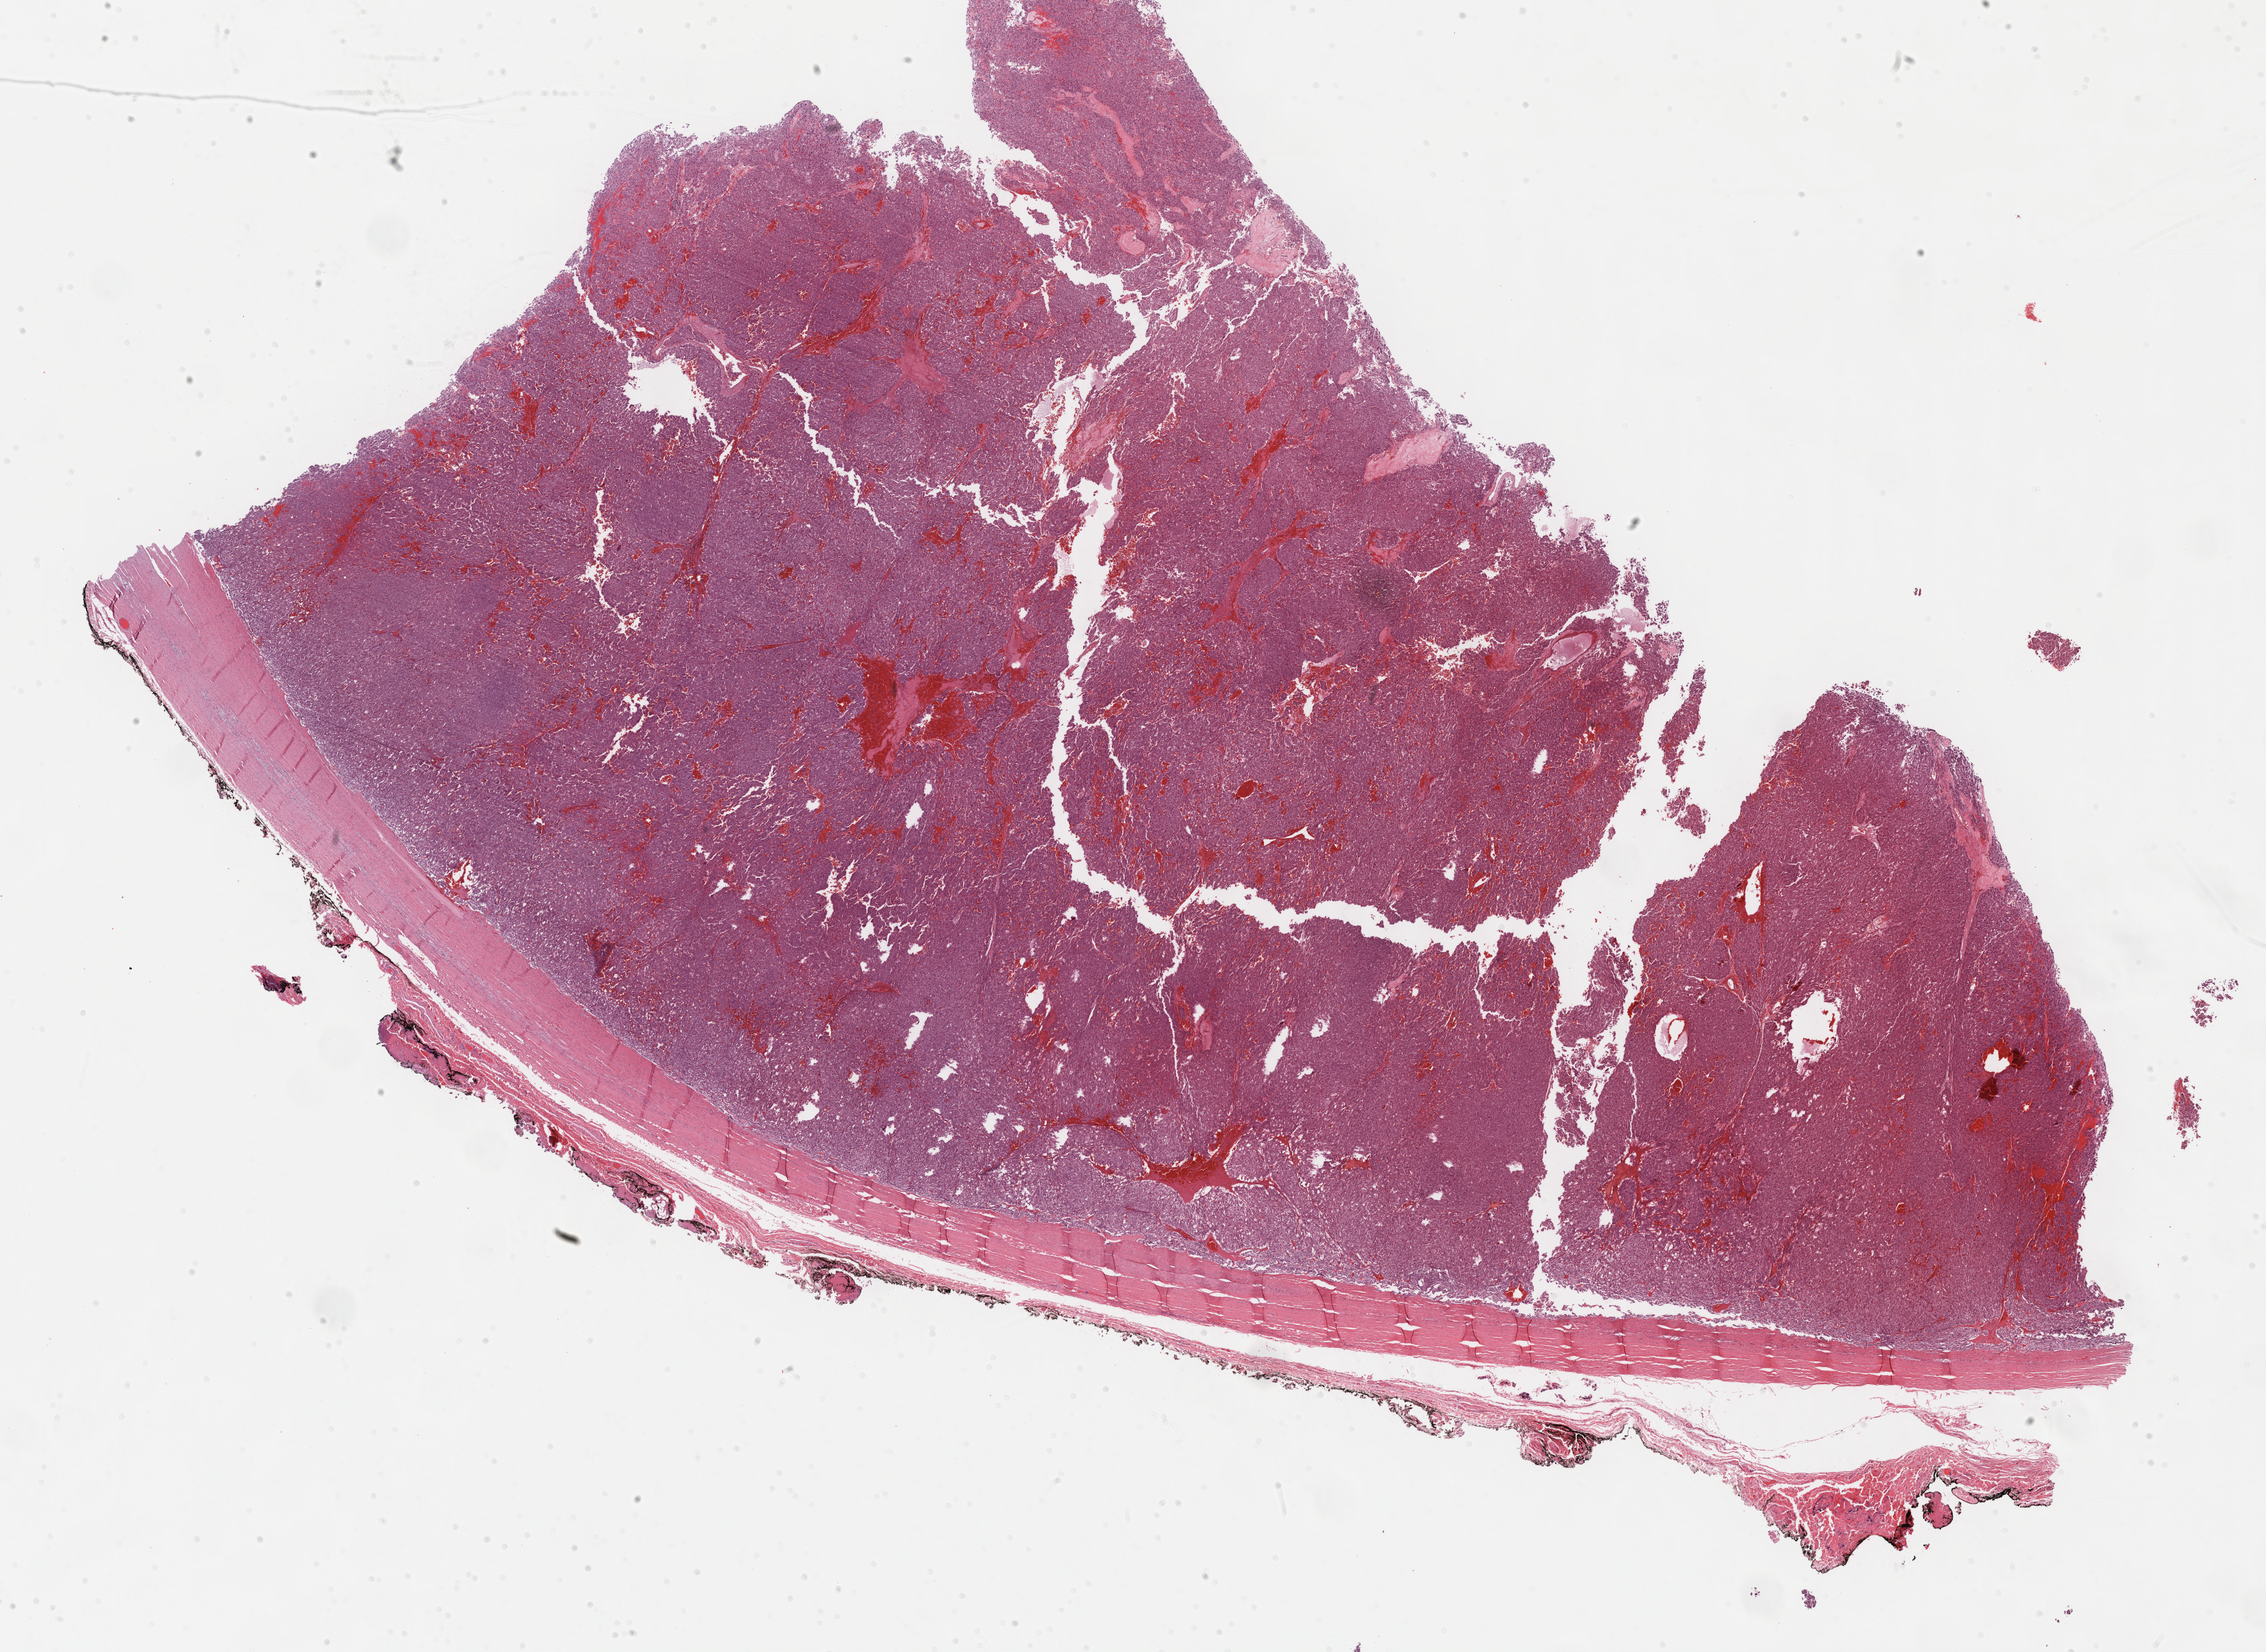
Digitized Hematoxylin and eosin (H&E) stained tissue section (whole slide) — a low-resolution overview of the entire scanned area, about 26.7 x 19.4 mm (from a 40x scan), formalin-fixed paraffin-embedded (FFPE) diagnostic section, sample: primary tumour, adrenal gland. Female, age 19 years at initial diagnosis.
Pathologic diagnosis: Medullary carcinoma, NOS.